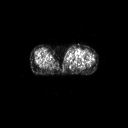
FDG PET of an extremity soft-tissue mass (from a PET/CT study), one axial slice; slice 48 of 91 in the series (ordered by position); 3.27 mm slice thickness; 128 × 128 image matrix, field of view 700 × 700 mm. Female patient, age 74 years. Case-level facts recorded for this patient, not image findings: histological type: pleomorphic leiomyosarcoma; grade: high; site of the primary tumour: left thigh.
Outlined on this slice (expert contour drawn on MRI and transferred to this co-registered scan by the dataset authors):
- gross tumour volume including surrounding oedema: bounding box [x1, y1, x2, y2] px = [65, 48, 77, 61]